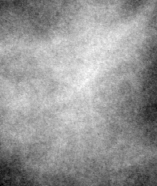
Crop from a digitized film mammogram around one marked abnormality, right breast, CC view.
Finding: mass, shape lobulated, margins circumscribed / ill defined; BI-RADS assessment category 4; pathology (as recorded): benign.